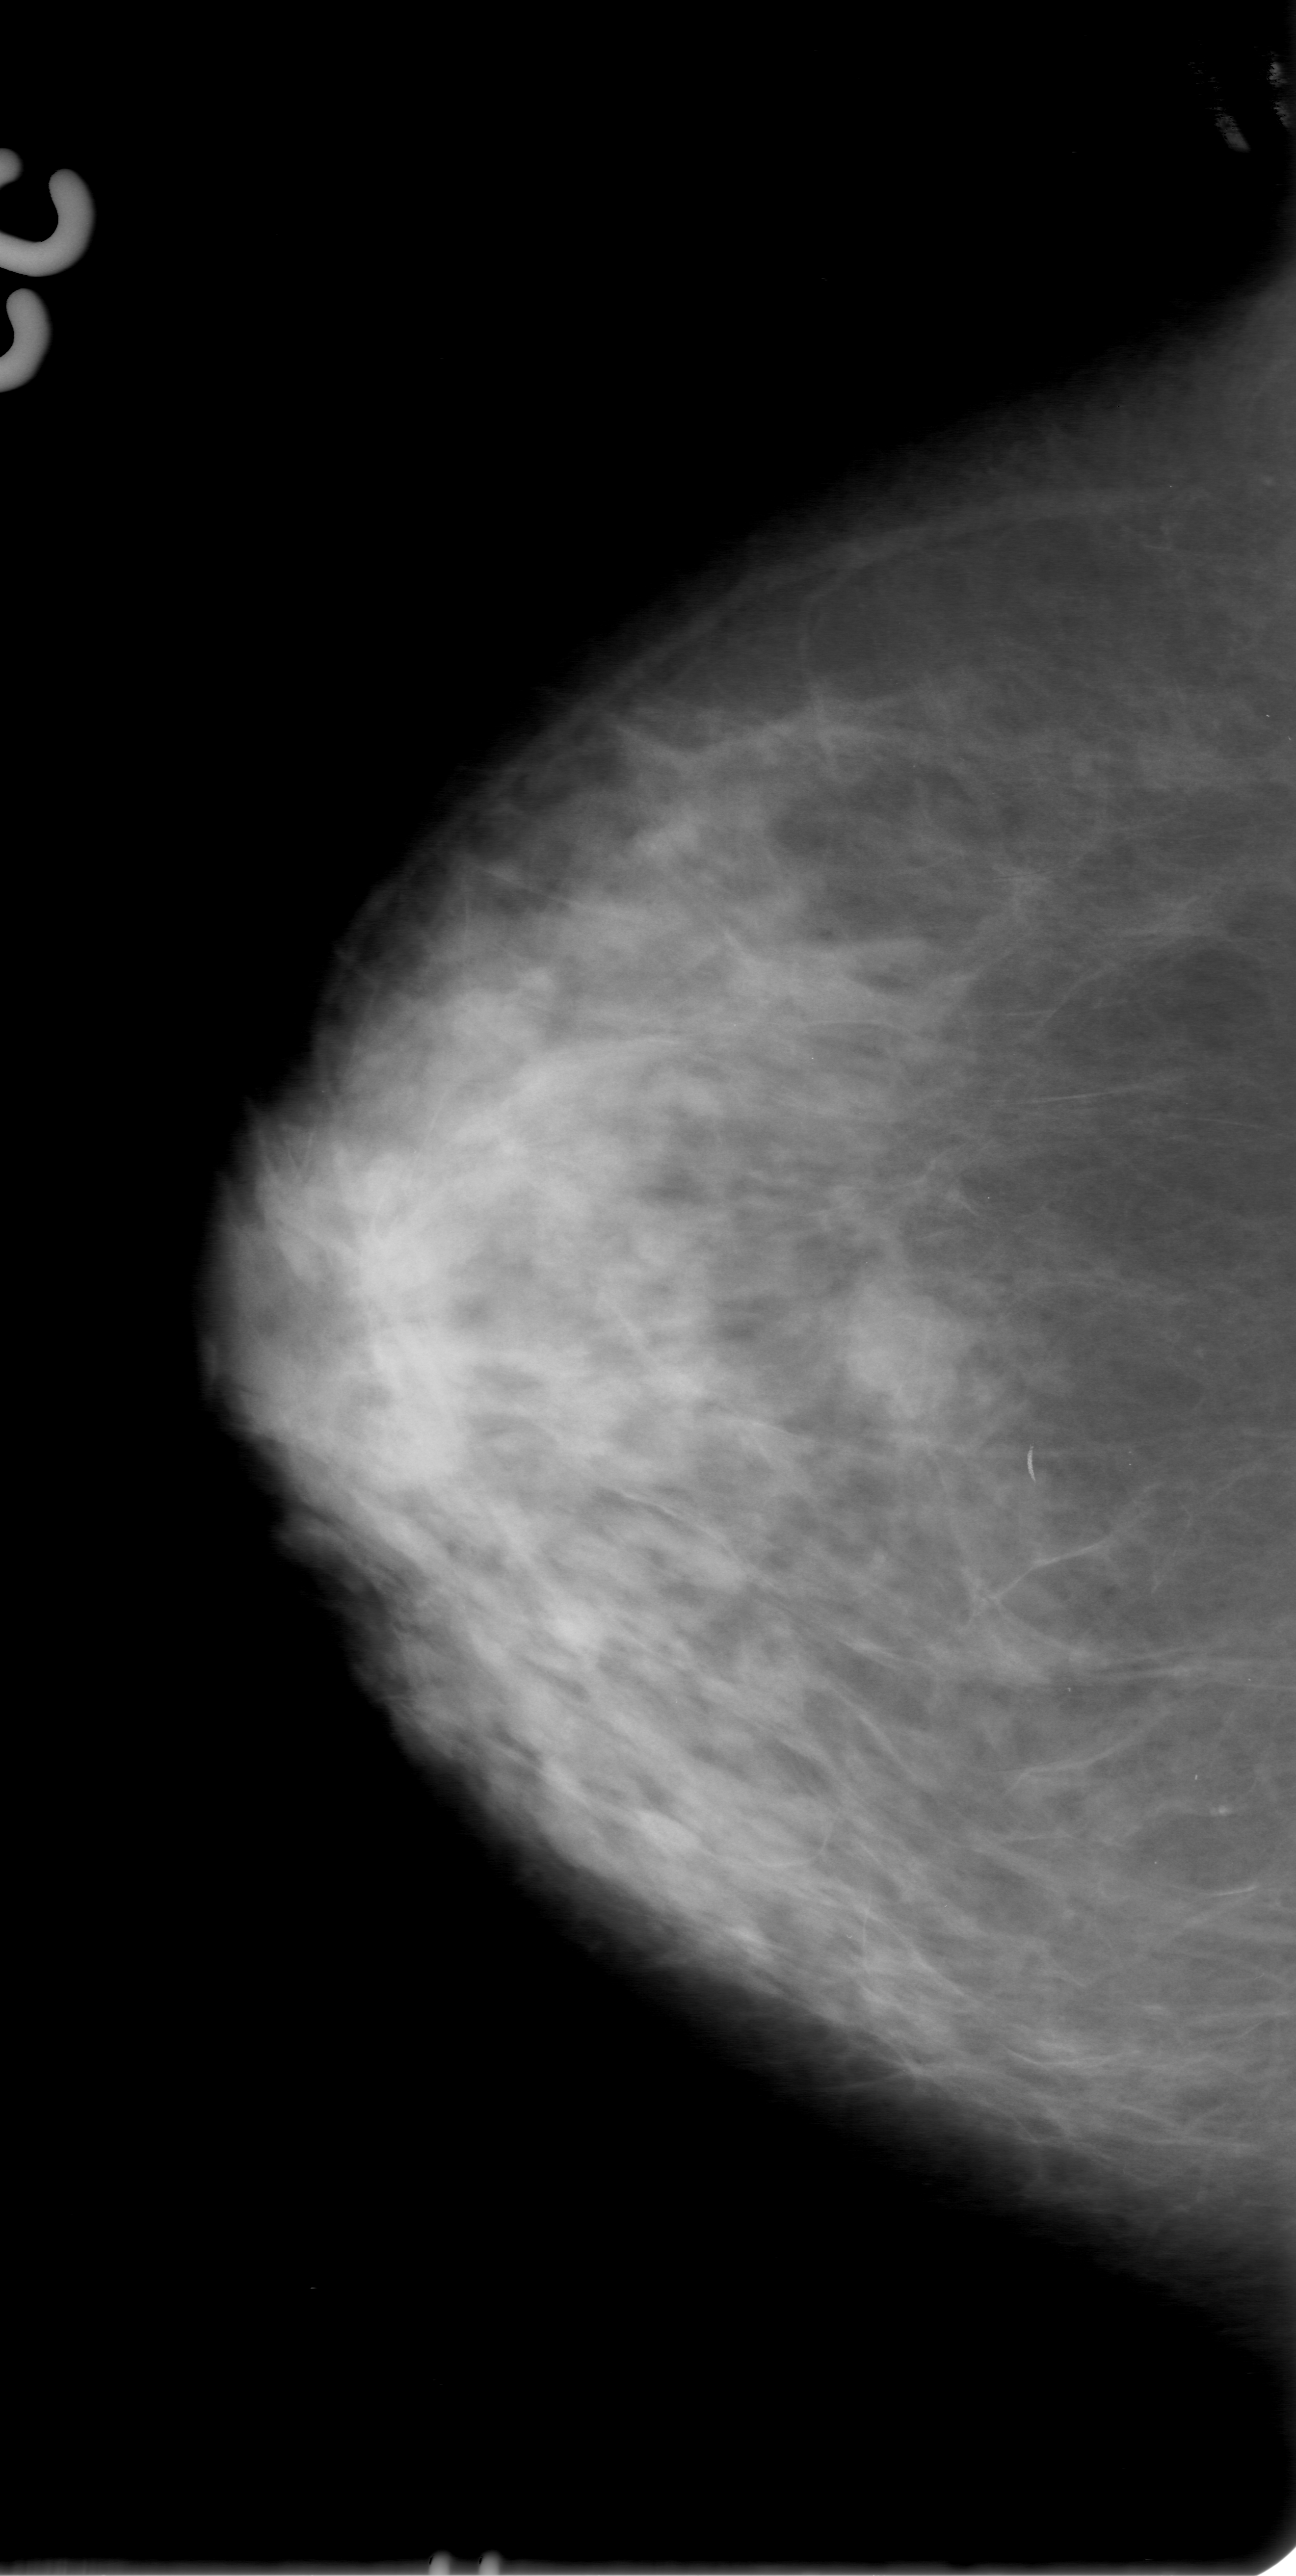
Mammogram (digitized film); right breast; CC view.
Abnormality record for this image: mass, shape lobulated, margins circumscribed; BI-RADS assessment category 0 (incomplete: needs additional imaging); pathology result (as recorded, not read from the image): malignant.